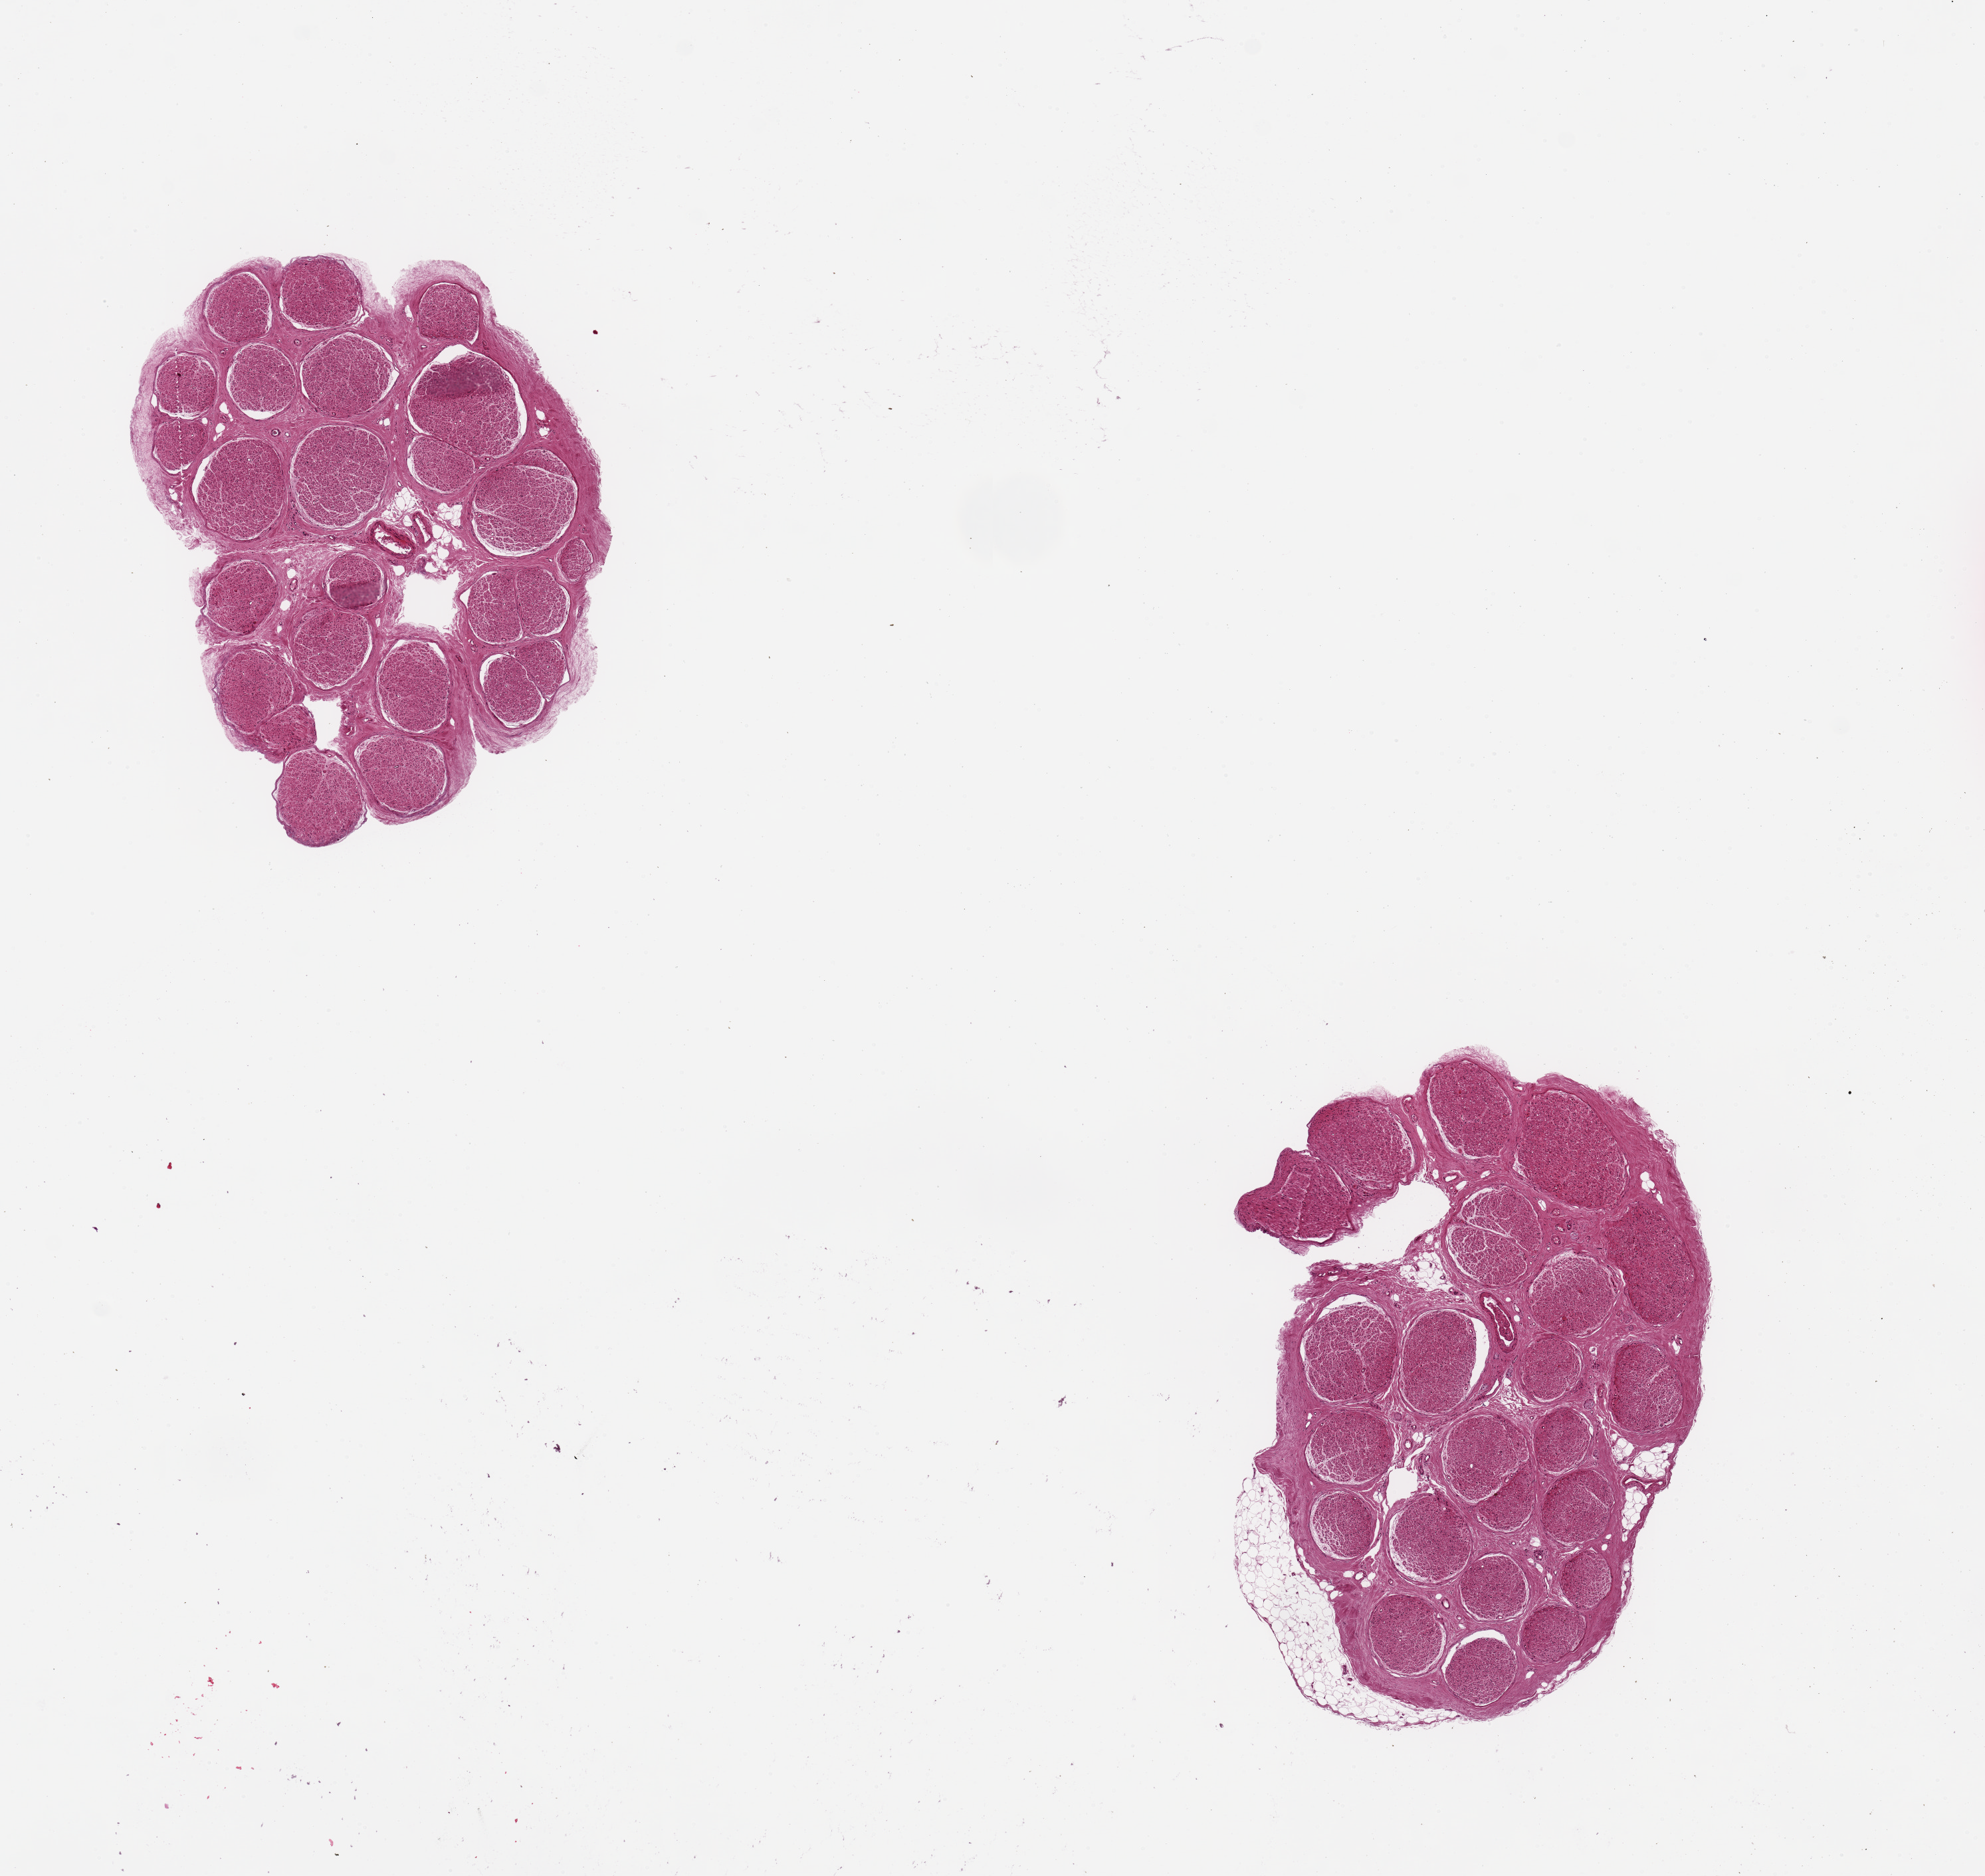
Whole-slide image, H&E stain — whole scanned area (about 11.8 x 11.2 mm, slide scanned at 20x) shown as a low-resolution overview. PAXgene-fixed, paraffin-embedded tissue. Sampled site (target tissue): tibial nerve. Donor tissue sample. Donor: male.
• review note (as recorded): 2 pieces, good clean specimens ~4mm d